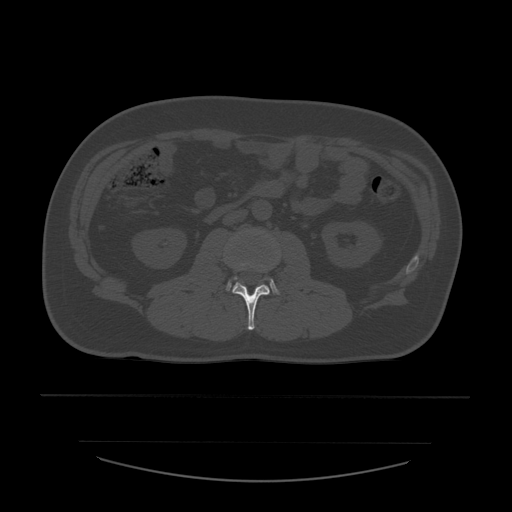
CT including the spine, one axial slice. Reconstruction kernel STANDARD. Bone window (W 1800 / L 400 HU). 1.25 mm slice thickness. 512 × 512 image matrix, field of view 441 × 441 mm. Patient age 44 years. Case-level facts recorded for this patient, not image findings: primary cancer: soft tissue sarcoma.
Annotated regions visible in this slice (semi-automatic segmentation, software-assisted and operator-edited):
- L2 vertebra: box from (x=233, y=269) to (x=270, y=331) px
- L3 vertebra: (x=227, y=263)–(x=278, y=293)